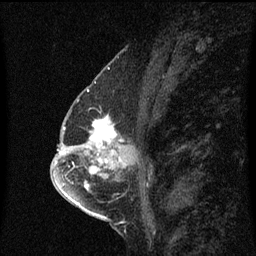
Breast MRI (dynamic contrast-enhanced), one sagittal slice. Position 35 of 60 along the scan axis. Dynamic contrast-enhanced series, image 2 of 3 at this slice position (ordered by acquisition). 1.5 T. TE 4.2 ms, TR 8.4 ms. 2 mm slice thickness. 256 × 256 image matrix, field of view 200 × 200 mm. Patient: female, 57 years. From the clinical record (not read from this slice): setting: breast cancer imaged before/during neoadjuvant chemotherapy; receptor status: HR-positive, HER2-negative.
Structures marked on this image (semi-automatic segmentation, software-assisted and operator-edited):
- analysis volume of interest (the breast-tissue region the enhancement analysis was run in; not a lesion): bounding box [x1, y1, x2, y2] px = [87, 116, 125, 145]
- tumour enhancement mask (voxels above the 70 % enhancement threshold inside the analysis volume of interest): [88, 116, 117, 145]